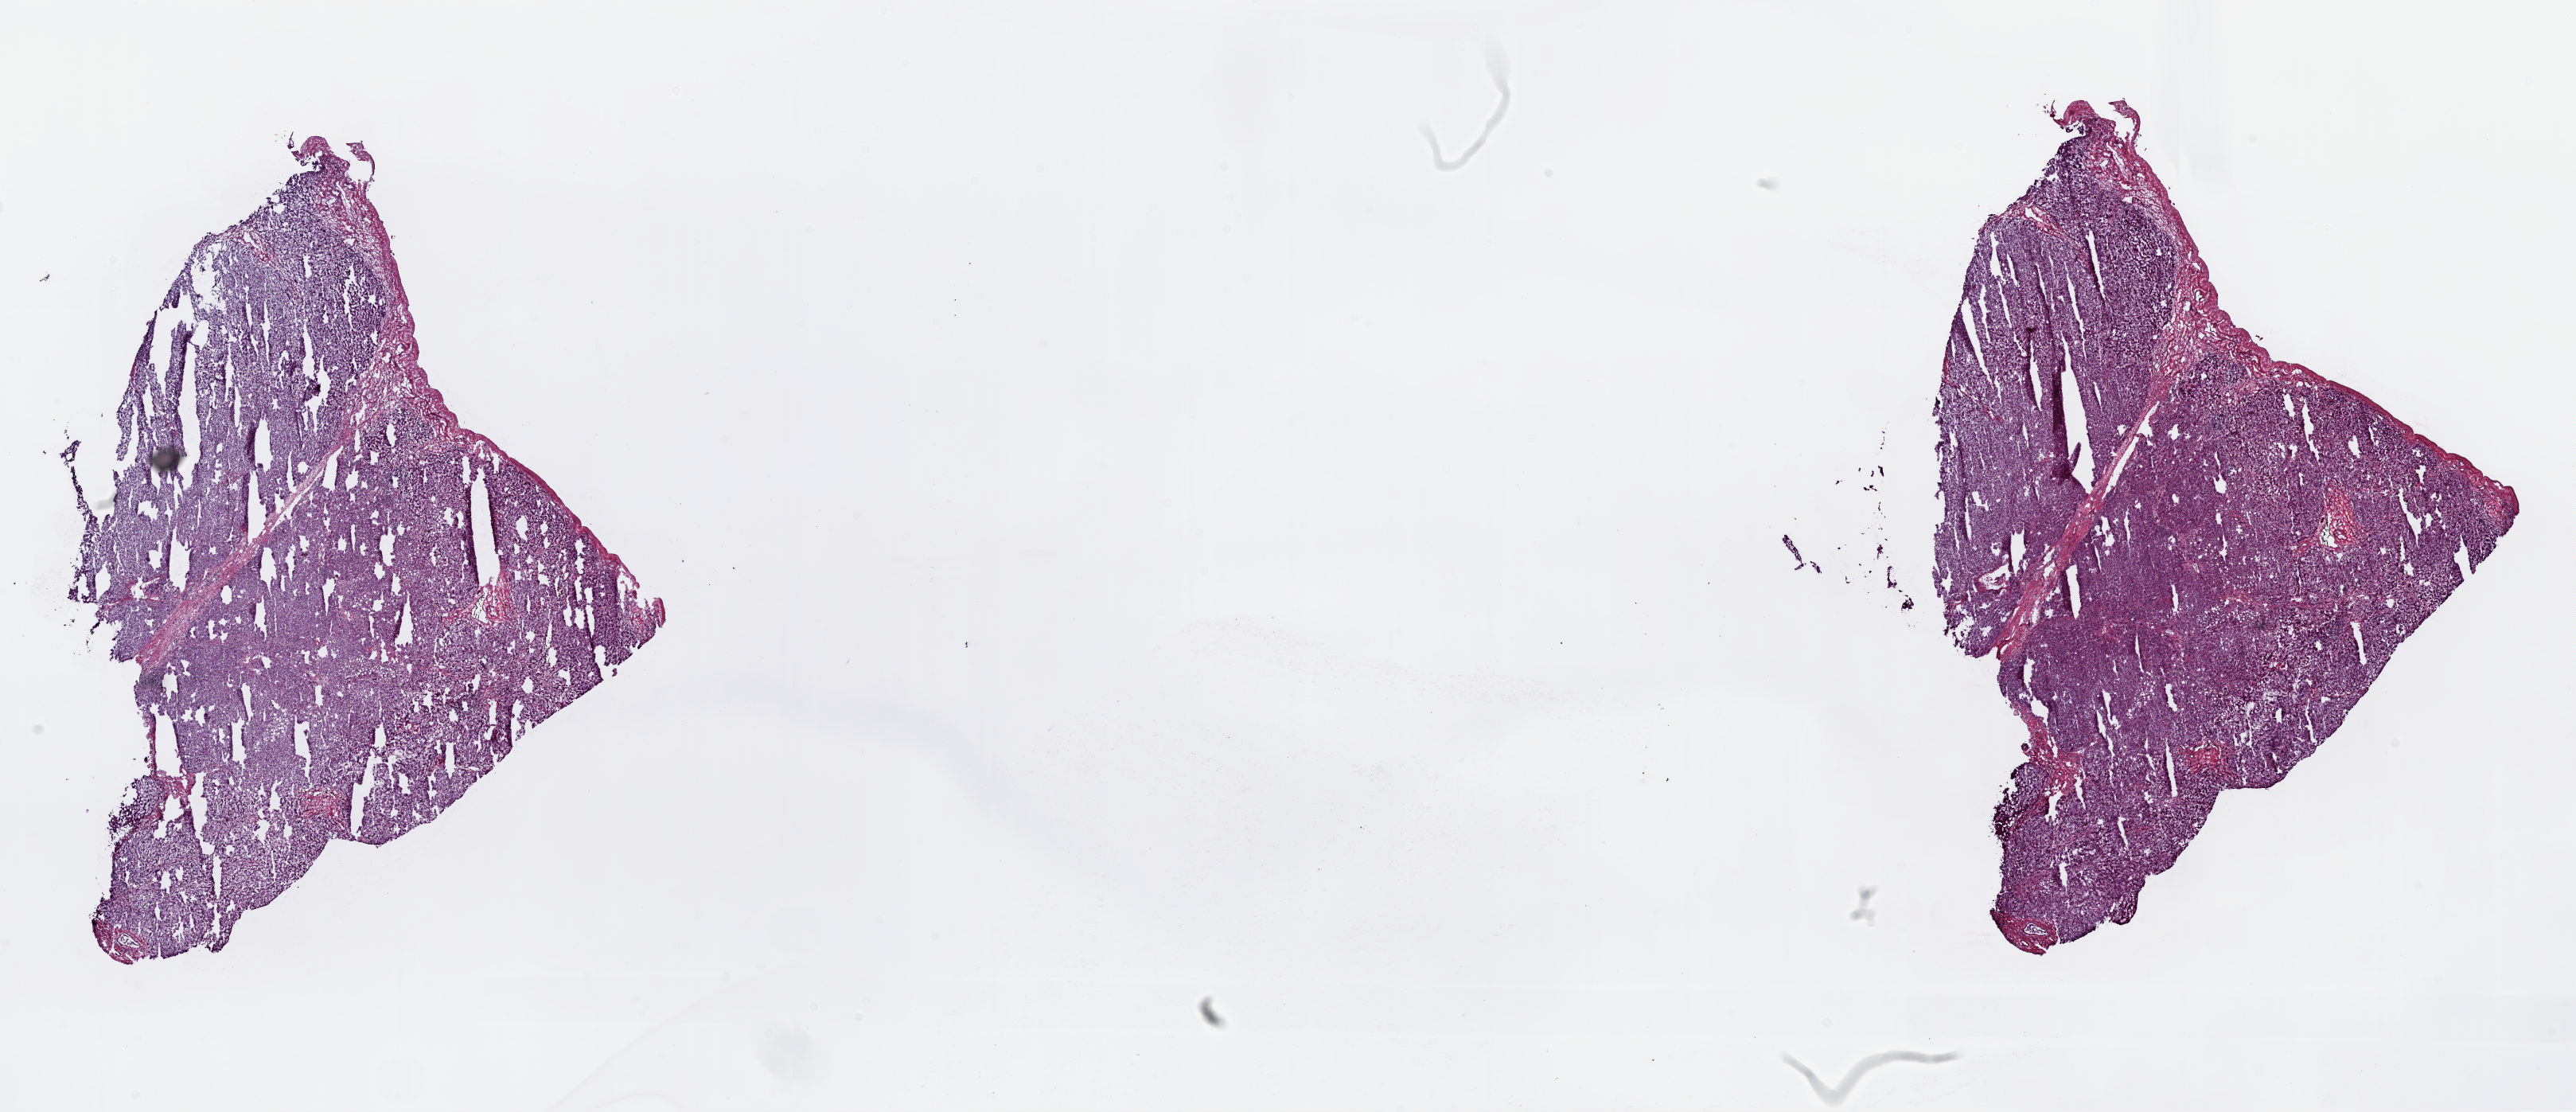
Digitized H&E-stained tissue section (whole slide), a low-resolution overview of the entire scanned area, about 25.6 x 11.1 mm (slide scanned at 20x); frozen section from the top of the tissue portion; sample: solid tissue normal (non-tumour tissue), liver. Patient: female, age at initial diagnosis 70 years. Composition of this section per pathologist review: tumour cells 0%, tumour nuclei 0%, normal cells 92%, stromal cells 8%, necrosis 0%. Infiltration values recorded for this section: lymphocyte infiltration 3%, monocyte infiltration 0%, neutrophil infiltration 0%.
* this section: solid tissue normal (non-tumour) sample from the same patient
* patient diagnosis: Hepatocellular carcinoma, NOS